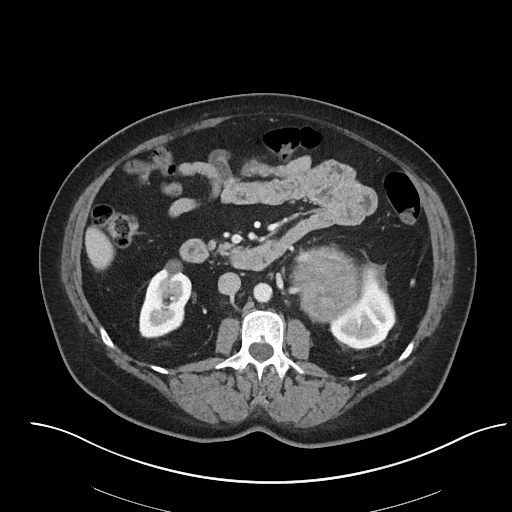
Contrast-enhanced abdominal CT, one axial slice; slice 31 of 92 in the series (ordered by position); reconstruction kernel I40f/2; soft-tissue window (W 400 / L 40 HU); 3 mm slice thickness; 512 × 512 image matrix, field of view 440 × 440 mm. Female patient, age 53 years. From the clinical record (not read from this slice): diagnosis: adrenocortical carcinoma; tumour side: left adrenal; tumour size at pathology: 9 cm; Ki-67 index: 28 %; stage (as recorded): 2.
Structures marked on this image (semi-automatically segmented with operator editing):
- mass: bounding box <292,248,360,320> (left, top, right, bottom; pixels)